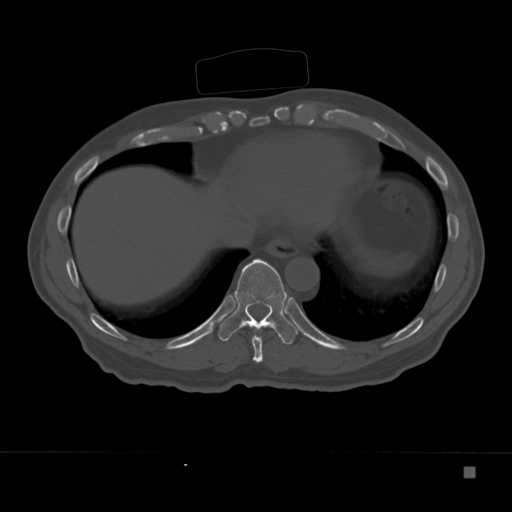
CT including the spine, one axial slice. Slice 177 of 332 in the series (ordered by position). 120 kVp. Bone window (W 1800 / L 400 HU). 1.5 mm slice thickness. 512 × 512 image matrix. Patient: male, 72 years. From the clinical record (not read from this slice): primary cancer: skeletal.
Outlined on this slice (semi-automatically segmented with operator editing):
- T10 vertebra: bounding box <218,259,298,344> (left, top, right, bottom; pixels)
- T9 vertebra: <238,323,263,363>